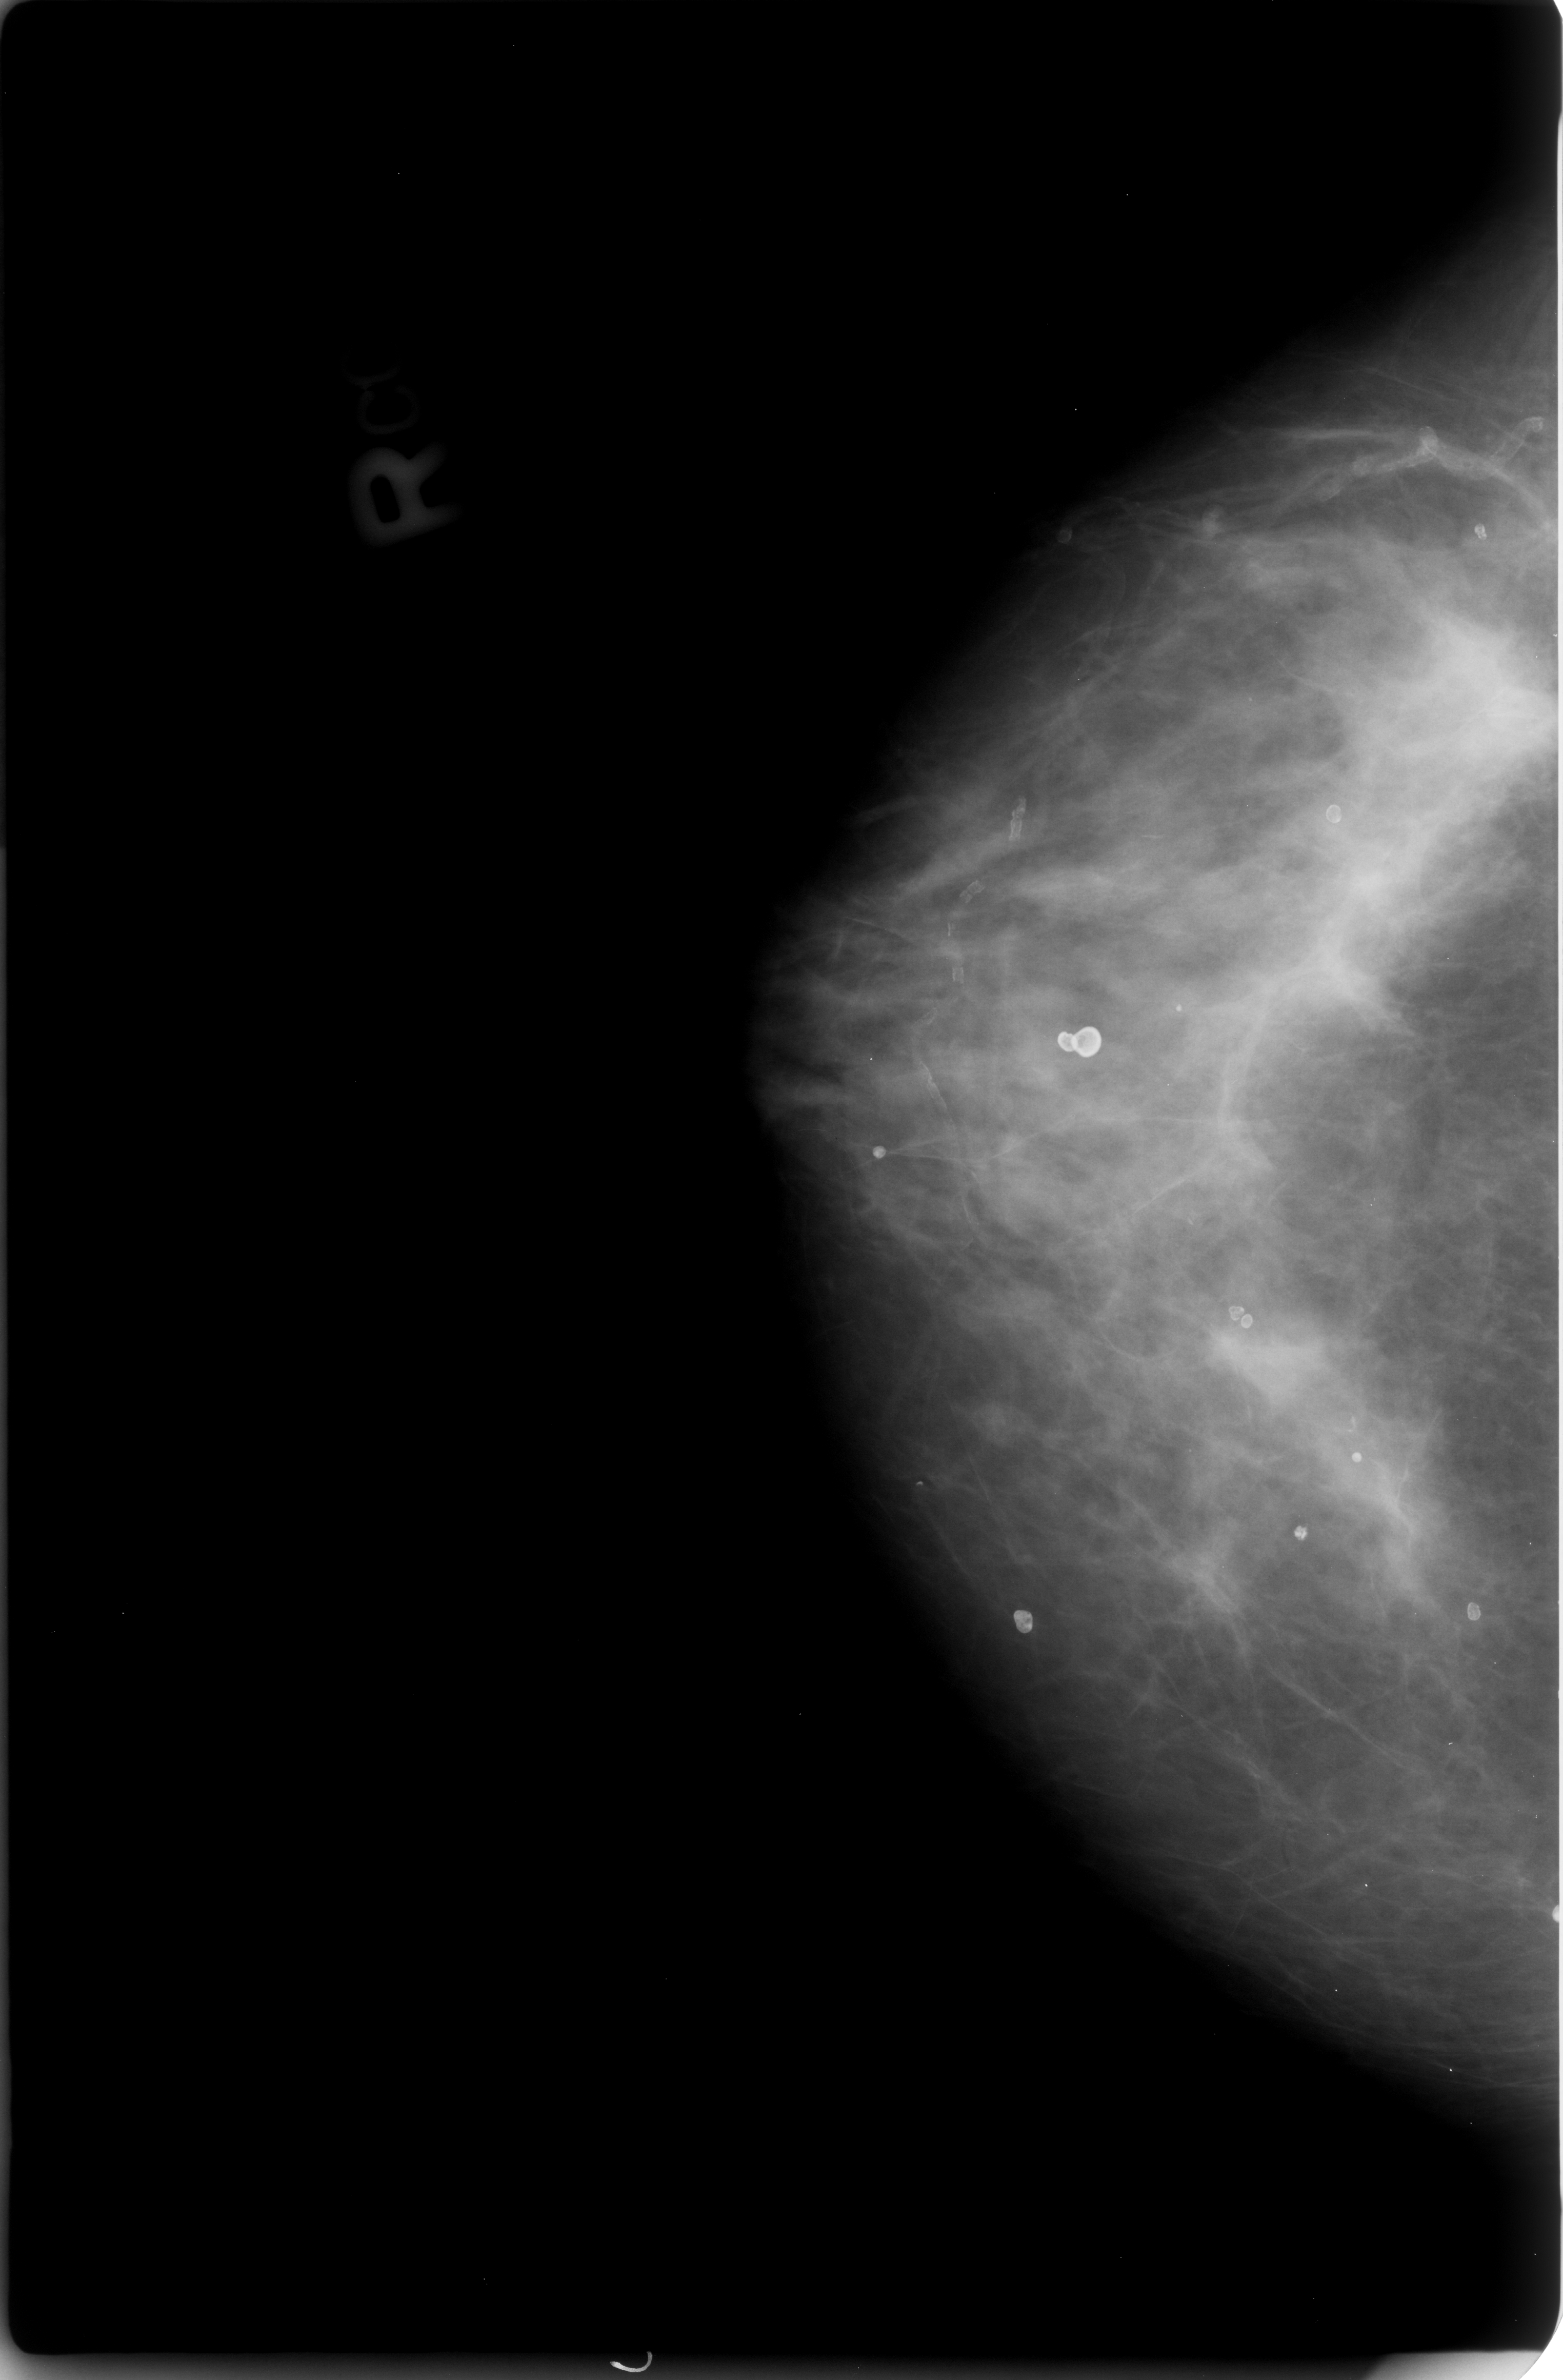
Digitized screen-film mammogram. Right breast. CC view. 1563 × 2380 image matrix.
Expert-marked regions of interest on this film, with their recorded descriptors:
- mass, shape irregular, margins obscured / ill defined; BI-RADS assessment category 4; pathology result (as recorded, not read from the image): benign: bounding box [x1, y1, x2, y2] px = [1438, 616, 1554, 801]